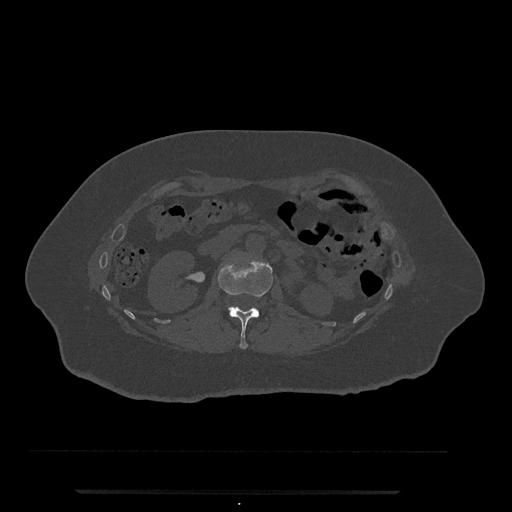
CT including the spine, one axial slice. Slice 90 of 797 in the series (ordered by position). Bone window (W 1800 / L 400 HU). 0.5 mm slice thickness. 512 × 512 image matrix. Patient: female, 51 years. Case-level facts recorded for this patient, not image findings: primary cancer: neuro; vertebrae with lytic lesions (as recorded): T8.
Structures marked on this image (semi-automatically segmented with operator editing):
- L1 vertebra: bounding box <218,256,273,349> (left, top, right, bottom; pixels)
- L2 vertebra: <228,306,233,311>